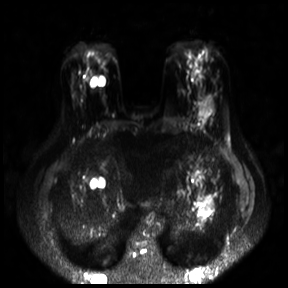
Breast MRI, one axial slice. Slice 10 of 30 in the series (ordered by position). Diffusion-weighted series; image 2 of 4 stored at this slice position (different b-values; order by instance number). 3 T. 288 × 288 image matrix, field of view 360 × 360 mm. Female patient.
Annotated regions visible in this slice (expert manual segmentation):
- tumour on diffusion-weighted imaging: bounding box <199,98,213,115> (left, top, right, bottom; pixels)